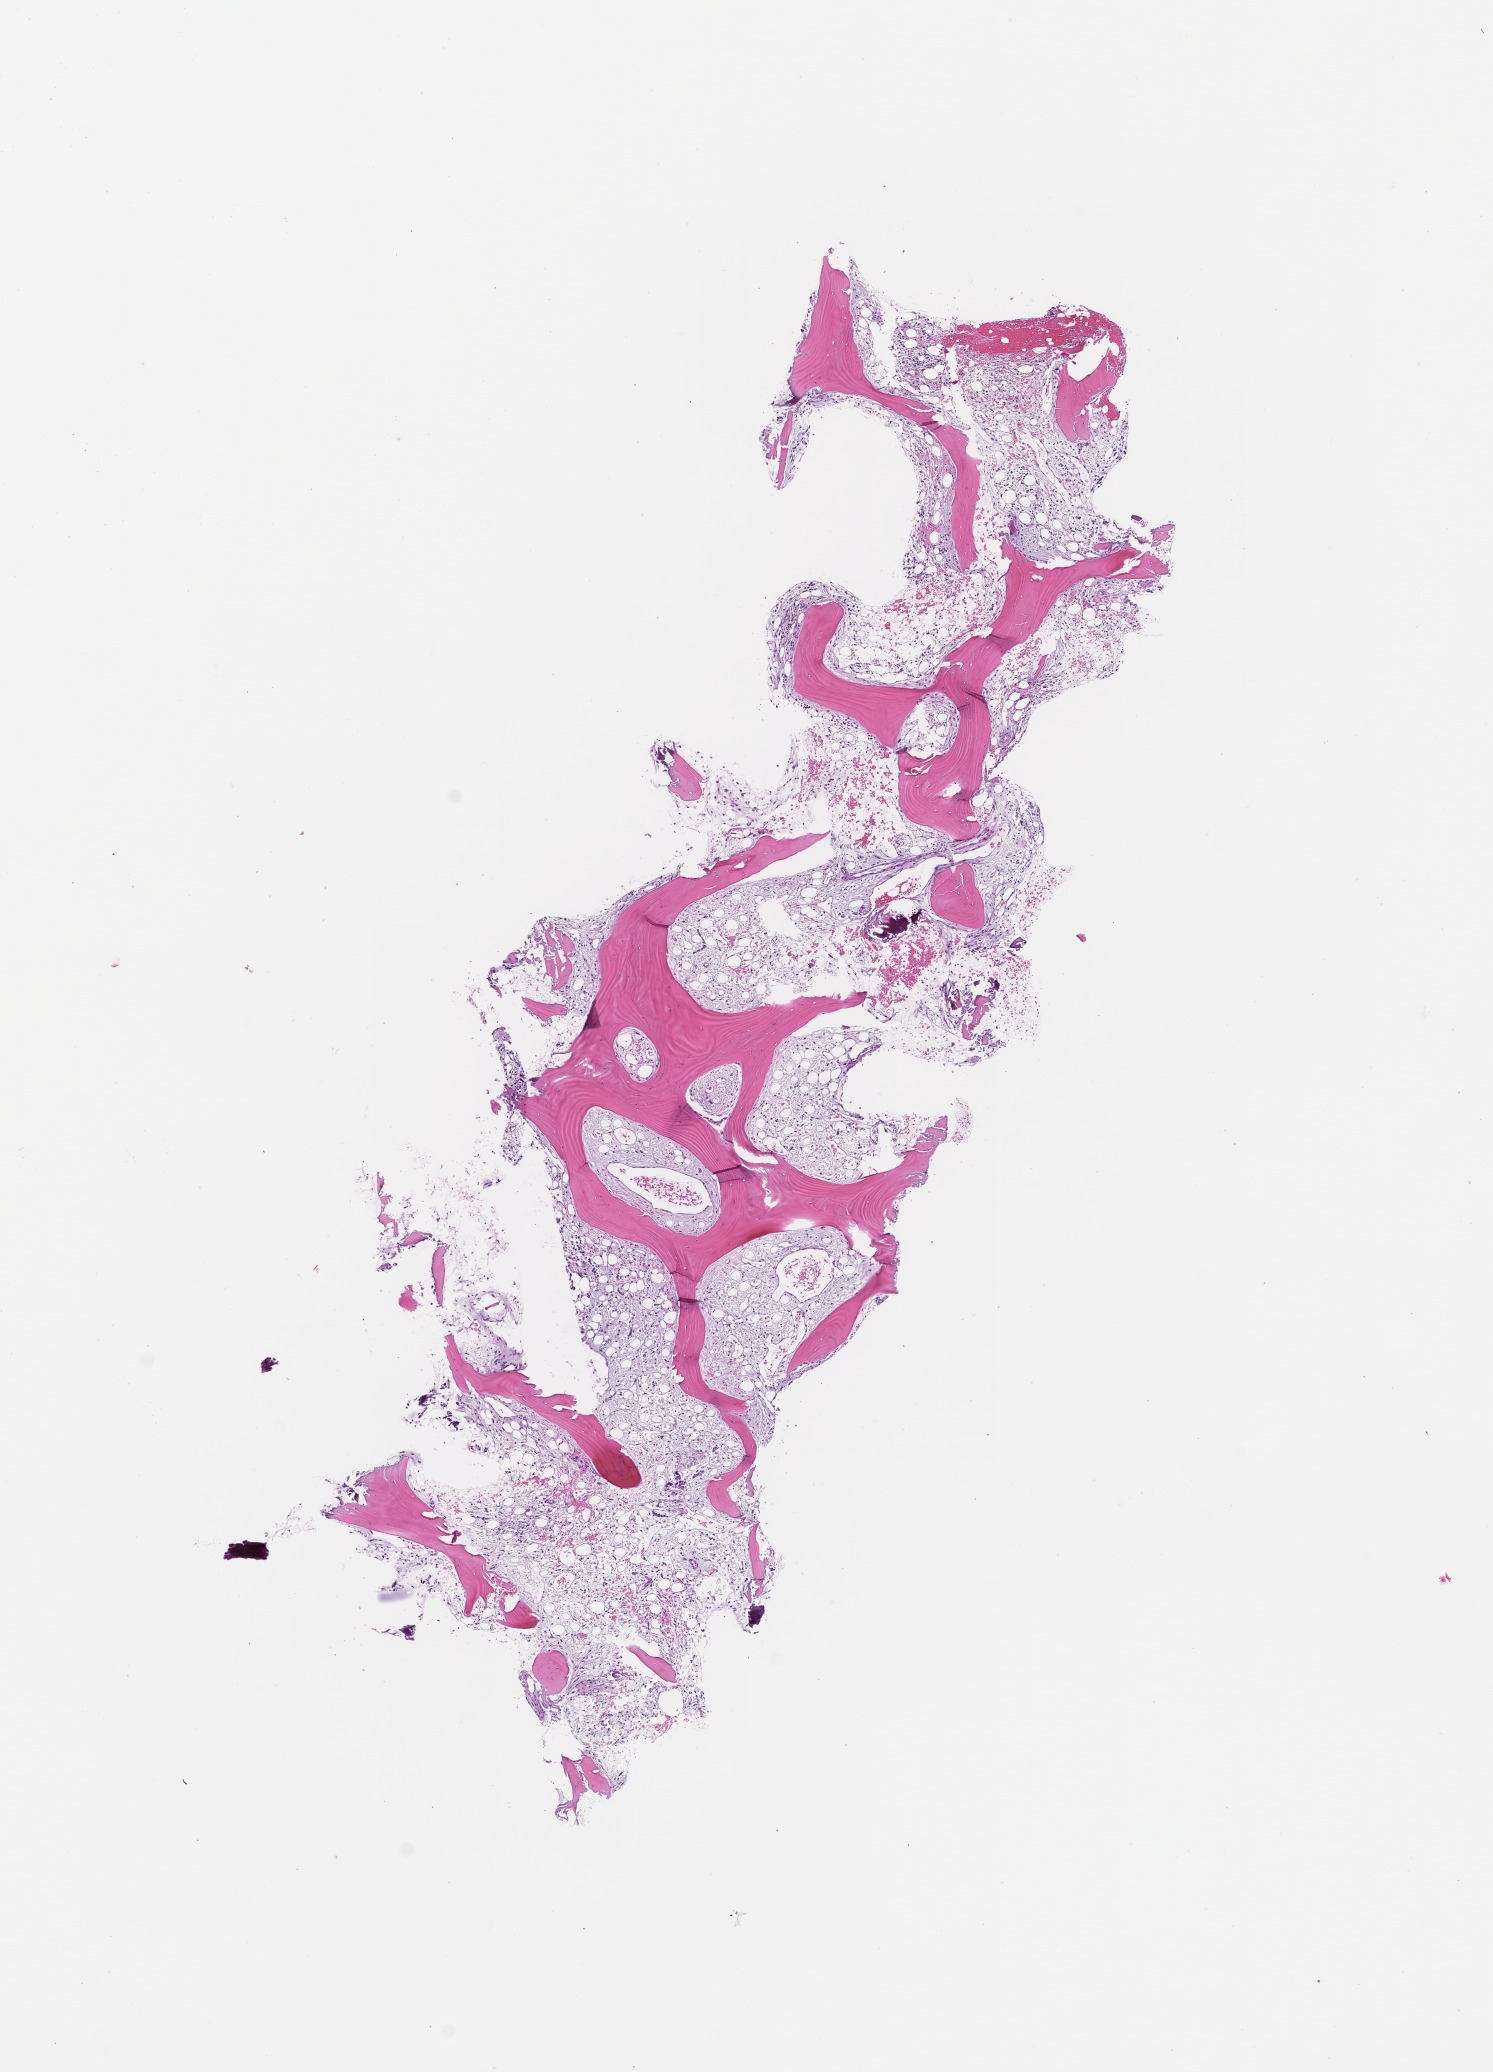
Whole-slide image, hematoxylin and eosin (H&E) stain, whole scanned area (about 6.0 x 8.4 mm) shown as a low-resolution overview, formalin-fixed paraffin-embedded section, site: bone marrow. Female patient.
This section: primary tumor. Diagnosis: Acute Myeloid Leukemia Not Otherwise Specified.